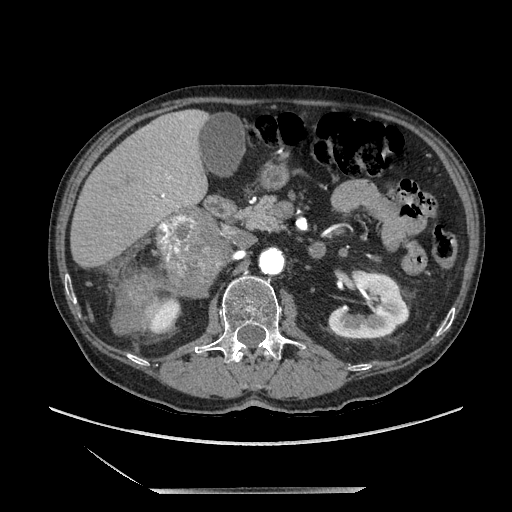
Contrast-enhanced abdominal CT, one axial slice; slice 101 of 243 in the series (ordered by position); soft-tissue window (W 400 / L 40 HU); 1.25 mm slice thickness; 512 × 512 image matrix, field of view 420 × 420 mm. Male patient. From the clinical record (not read from this slice): diagnosis: adrenocortical carcinoma; tumour side: right adrenal; tumour size at pathology: 16 cm; Ki-67 index: 17 %; stage (as recorded): 3.
Outlined on this slice (semi-automatic segmentation, software-assisted and operator-edited):
- mass: bounding box (x1, y1, x2, y2) in pixels: (161, 210, 223, 293)